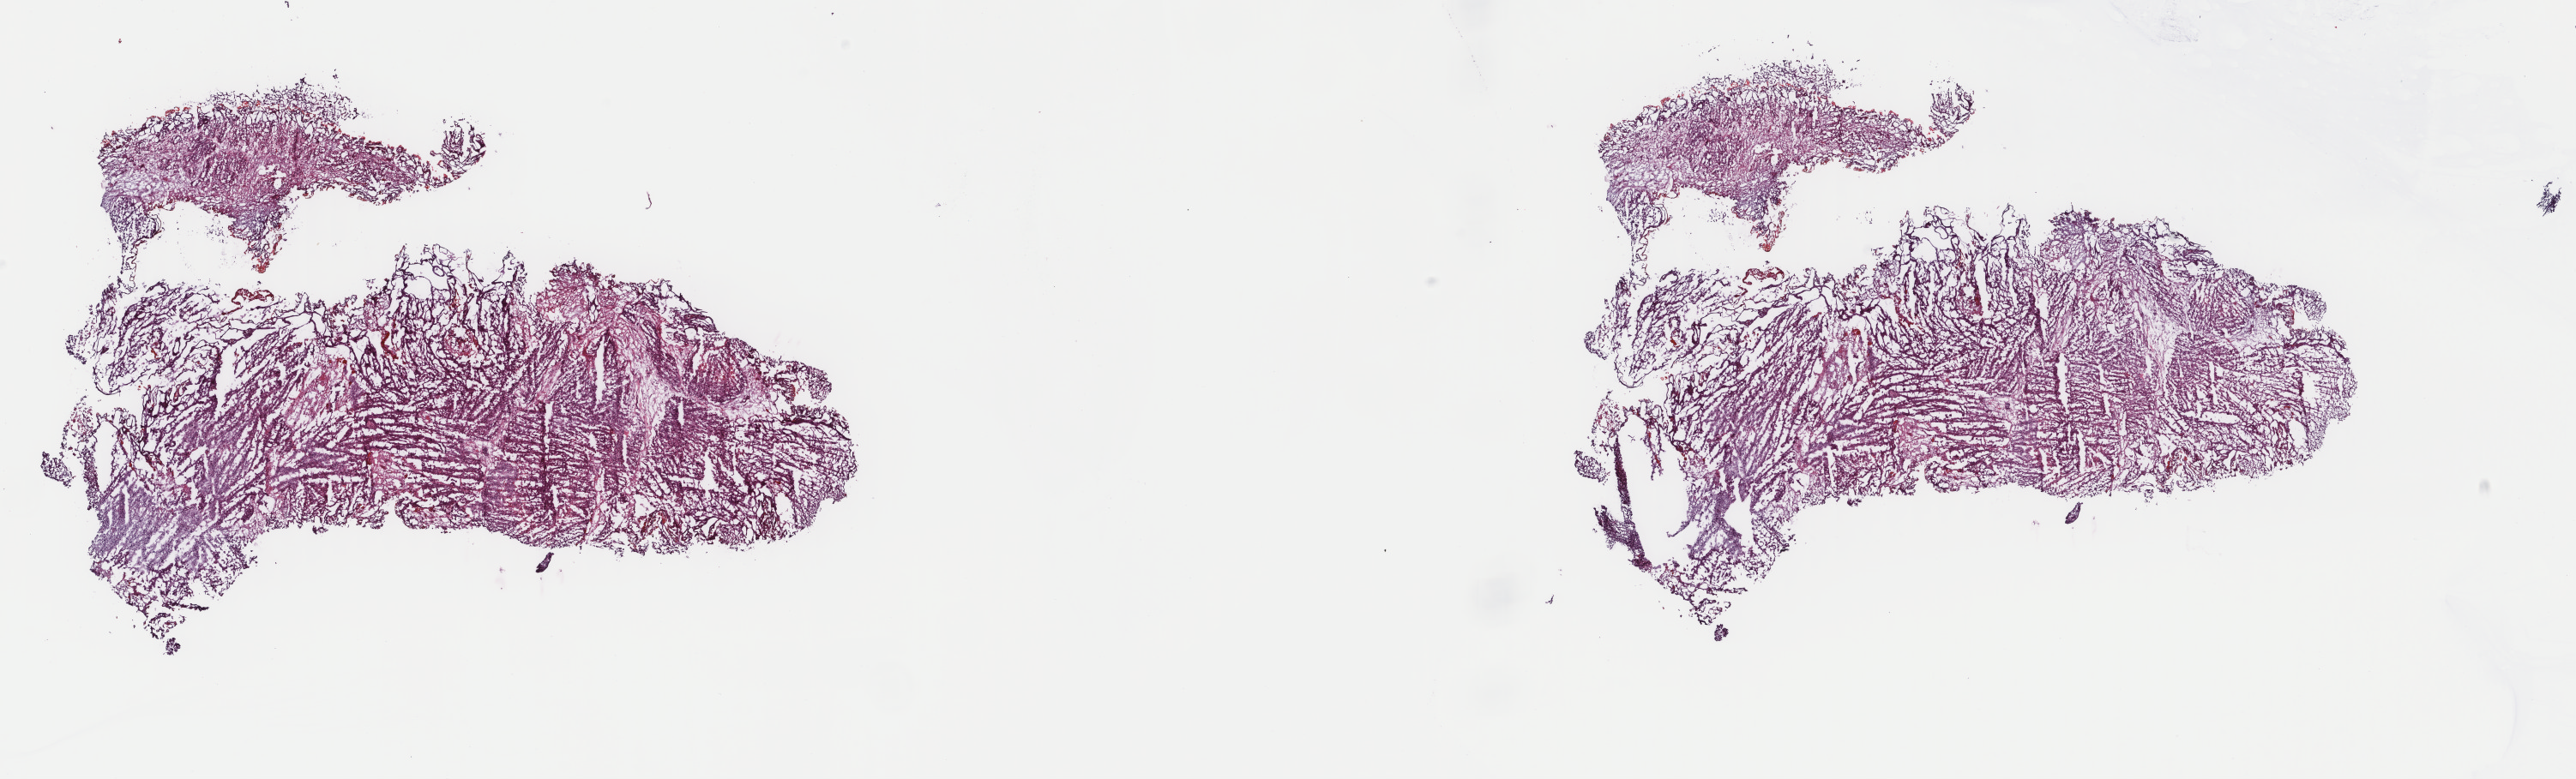
Whole-slide histology image, Hematoxylin and eosin (H&E) stained, whole scanned area (about 23.8 x 7.2 mm, from a 40x scan) shown as a low-resolution overview. Frozen section from the top of the tissue portion. Bladder, primary tumour sample. Male patient; age at initial diagnosis 74 years. Histologic grade: high grade. Composition of this section per pathologist review: tumour cells 95%, tumour nuclei 90%, normal cells 0%, stromal cells 0%, necrosis 5%. Inflammatory infiltration, as recorded: lymphocyte infiltration 3%, monocyte infiltration 0%, neutrophil infiltration 0%.
• AJCC pathologic stage: II (7th edition)
• pathologic diagnosis: Transitional cell carcinoma
• TNM: T2 NX MX